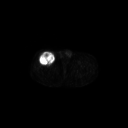
FDG PET of an extremity soft-tissue mass (from a PET/CT study), one axial slice. Position 286 of 311 along the scan axis. 3.27 mm slice thickness. 128 × 128 image matrix. Patient: male, 56 years. From the clinical record (not read from this slice): histological type: pleiomorphic leiomyosarcoma; grade: intermediate; site of the primary tumour: right thigh.
Structures marked on this image (expert contour drawn on MRI and transferred to this co-registered scan by the dataset authors):
- gross tumour volume including surrounding oedema: bounding box (x1, y1, x2, y2) in pixels: (38, 52, 55, 65)
- gross tumour volume (mass): (38, 52, 55, 65)